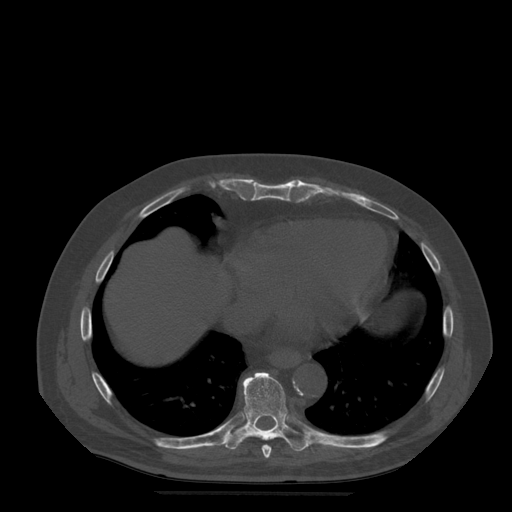
CT including the spine, one axial slice; slice 295 of 522 in the series (ordered by position); bone window (W 1800 / L 400 HU); 1.25 mm slice thickness; 512 × 512 image matrix. Patient age 72 years. Case-level facts recorded for this patient, not image findings: primary cancer: prostate.
Structures marked on this image (semi-automatic segmentation, software-assisted and operator-edited):
- T8 vertebra: box from (x=262, y=445) to (x=272, y=459) px
- T9 vertebra: (x=224, y=372)–(x=310, y=452)